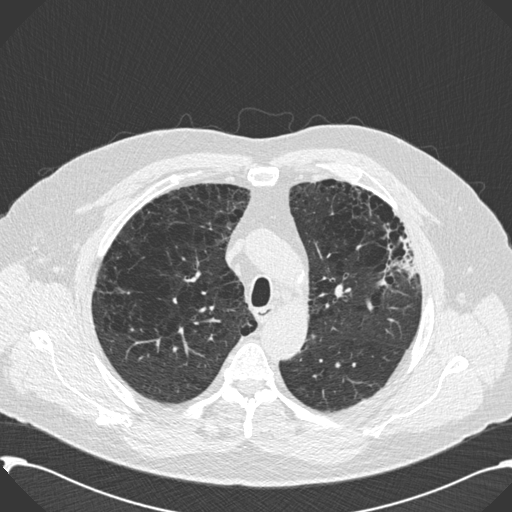
Axial slice from a low-dose chest CT screening exam; second screening round (one year after baseline); lung window (W 1500 / L -600 HU); 2 mm slice thickness; 120 kVp; slice 47 of 199 in the series; 512 × 512 image matrix, field of view 380 × 380 mm. Male, age 59 years at enrolment.
- Expert-annotated lung lesion, box from (x=363, y=208) to (x=422, y=296) px.
- Screening reader's record for this exam: no non-calcified nodule ≥4 mm recorded.
- Official screen result: negative screen, significant abnormalities not suspicious for lung cancer.
- Lung cancer was diagnosed 518 days after this screen (after the third annual screen): bronchiolo-alveolar carcinoma, mixed mucinous and non-mucinous, left upper lobe, stage IA (AJCC 6th edition), 20 mm at pathology.